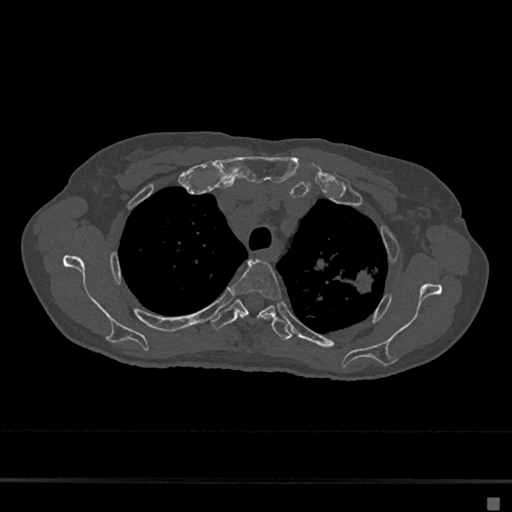
CT including the spine, one axial slice. Position 523 of 797 along the scan axis. Reconstruction kernel Br40s/3. 120 kVp. Bone window (W 1800 / L 400 HU). 512 × 512 image matrix, field of view 360 × 360 mm. Patient: female, 68 years. From the clinical record (not read from this slice): primary cancer: renal.
Outlined on this slice (semi-automatically segmented with operator editing):
- T3 vertebra: bounding box <230,259,281,320> (left, top, right, bottom; pixels)
- T4 vertebra: <210,299,292,341>